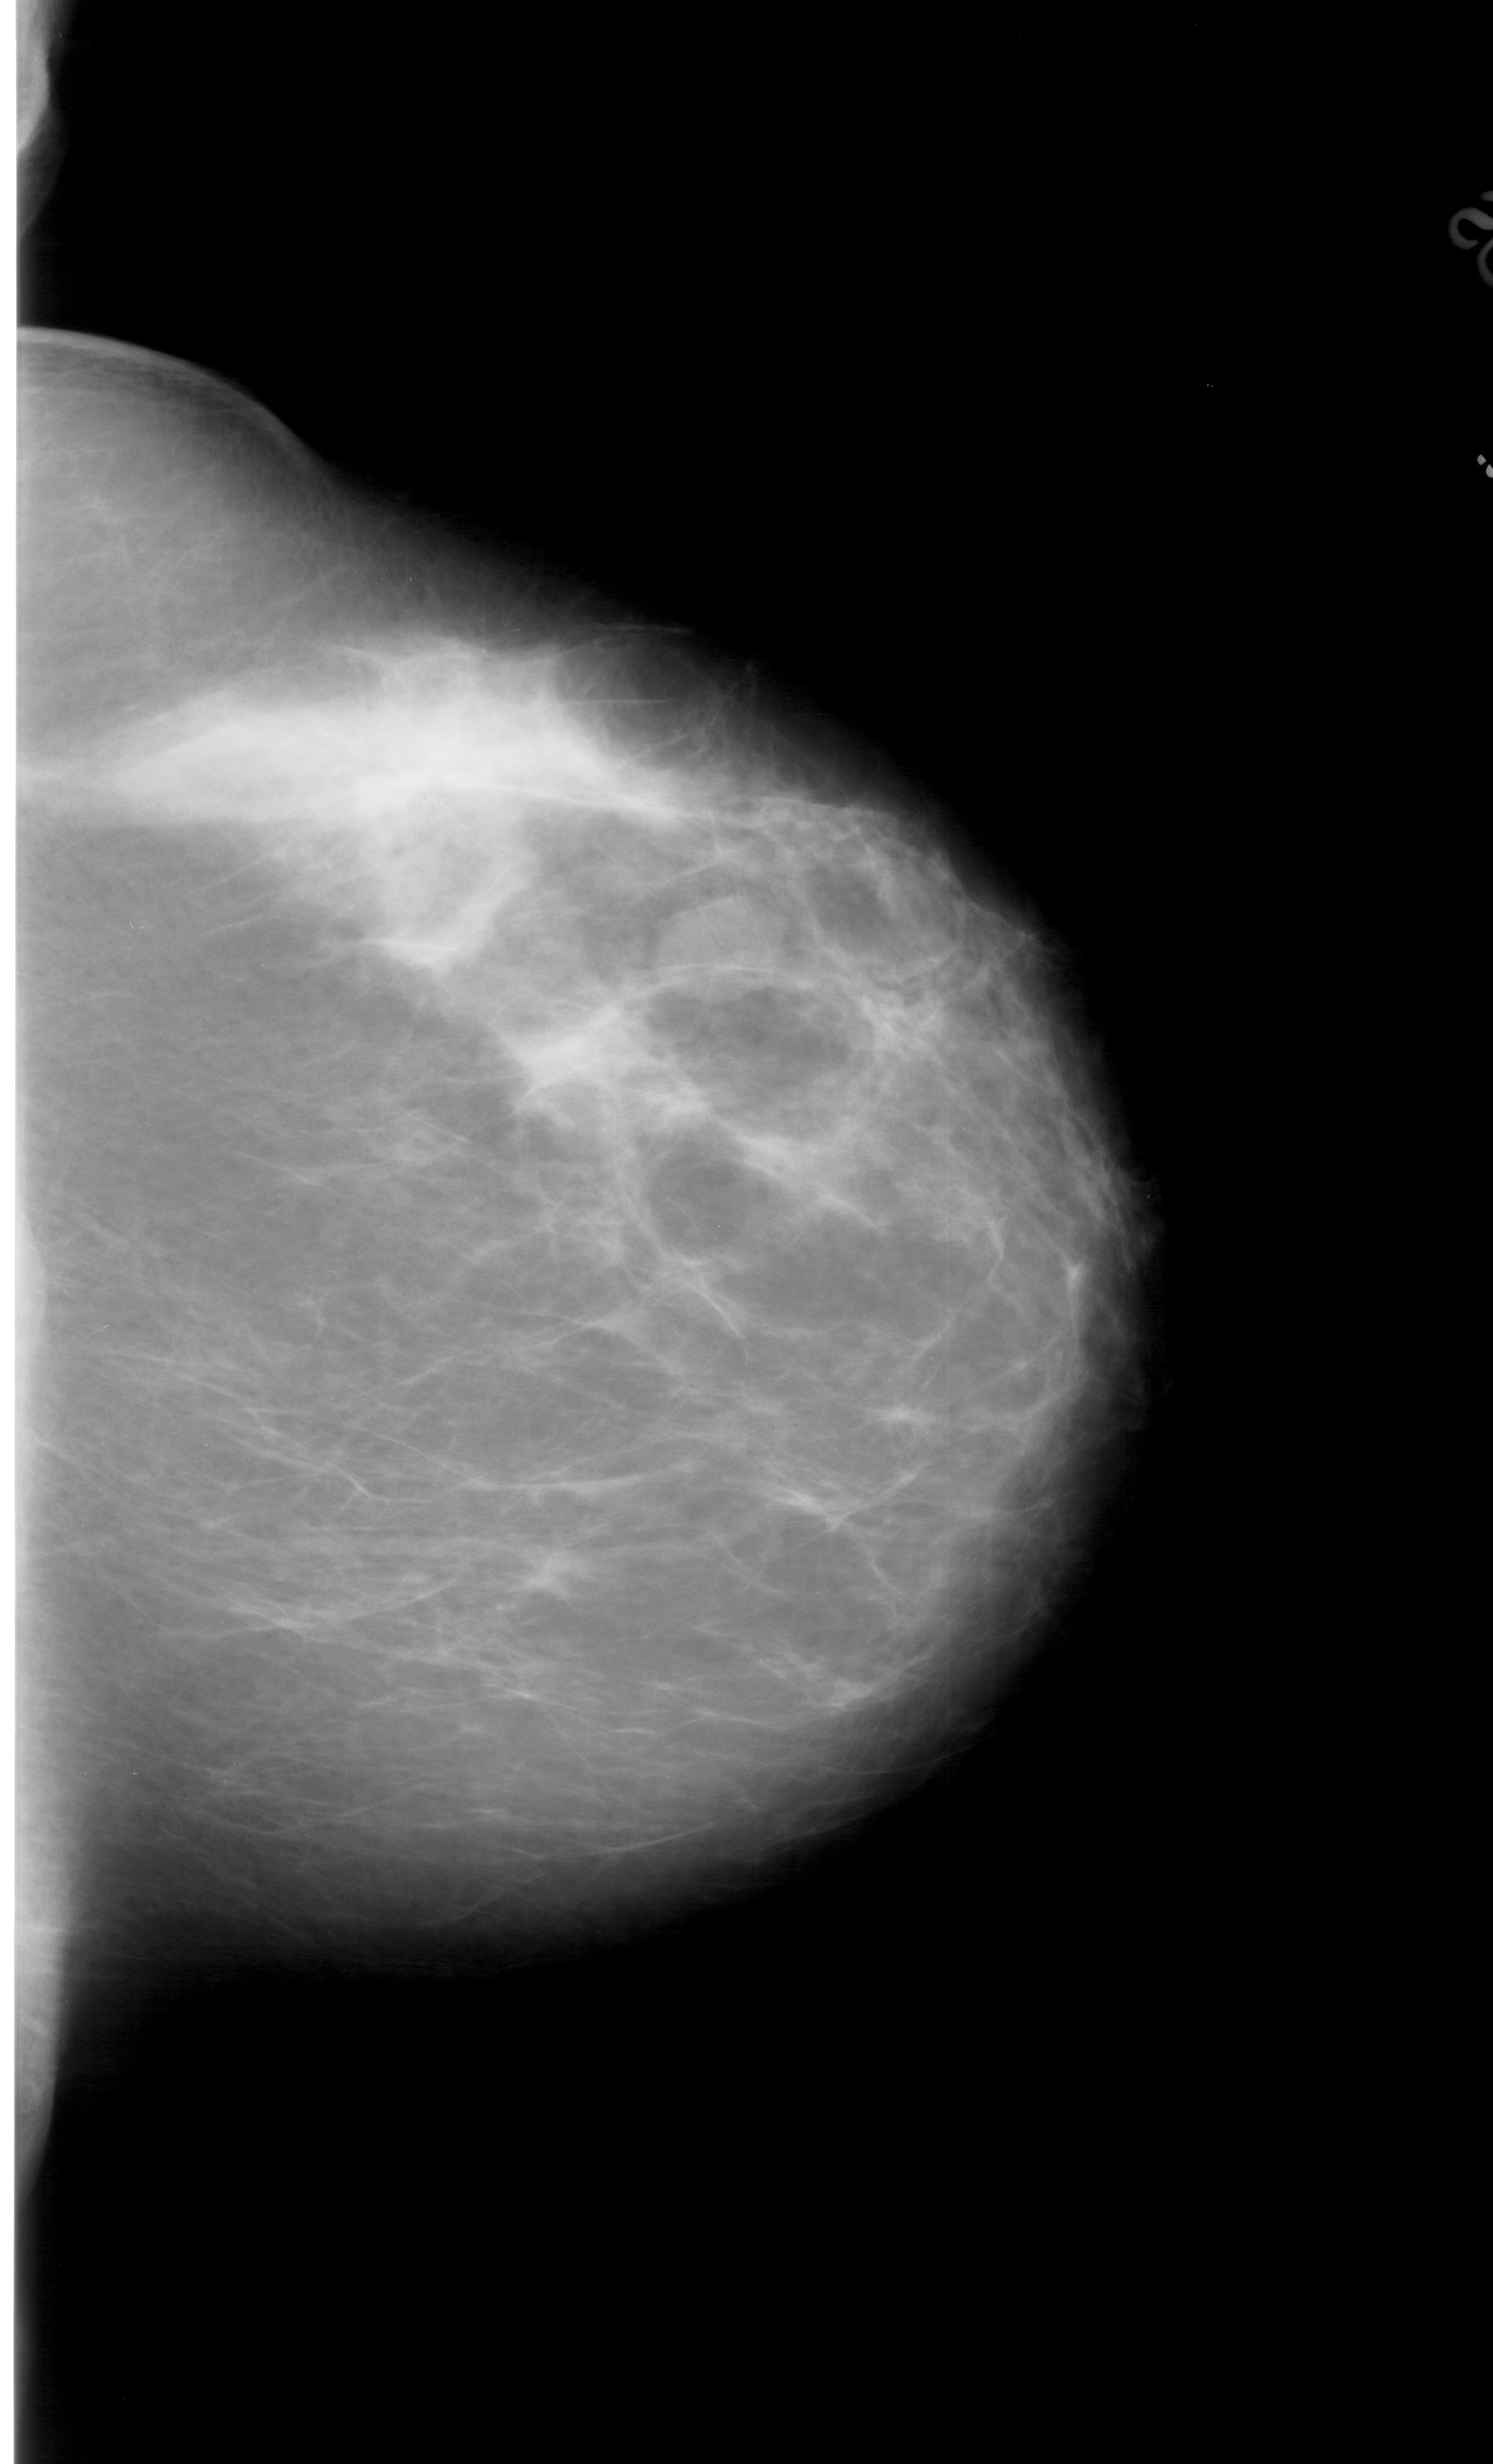
Scanned film-screen mammogram; right breast; CC view; BI-RADS breast density category 2 (scale 1–4).
- Abnormality record for this image: mass, shape oval, margins circumscribed; BI-RADS assessment category 3; pathology (as recorded): benign.